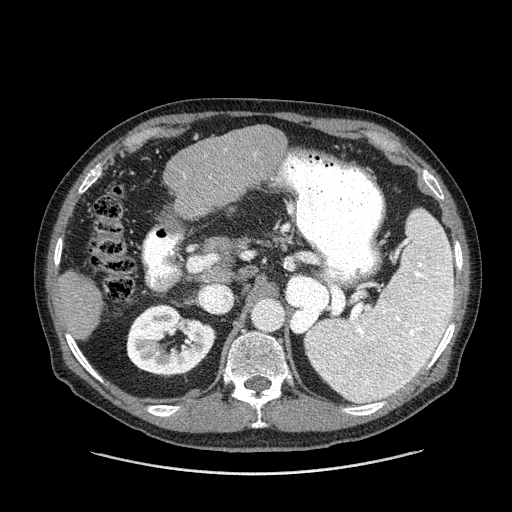
Contrast-enhanced abdominal CT (liver protocol), one axial slice. Slice 74 of 180 in the series (ordered by position). Reconstruction kernel STANDARD. 120 kVp. One of 2 acquisitions stored at this slice position. Soft-tissue window (W 400 / L 40 HU). 2.5 mm slice thickness. 512 × 512 image matrix, field of view 420 × 420 mm. From the clinical record (not read from this slice): diagnosis: hepatocellular carcinoma (patient treated with transarterial chemoembolisation; whether this scan precedes or follows treatment is not stated here); TNM stage (as recorded): Stage-II; Child-Pugh class: A; tumour size: 2.8 cm.
Outlined on this slice (semi-automatically segmented with operator editing):
- liver parenchyma outside the tumour (the mass and vessels are separate outlines, so this box may not span the whole liver): box from (x=54, y=125) to (x=286, y=340) px
- liver vessels: (x=183, y=154)–(x=256, y=178)